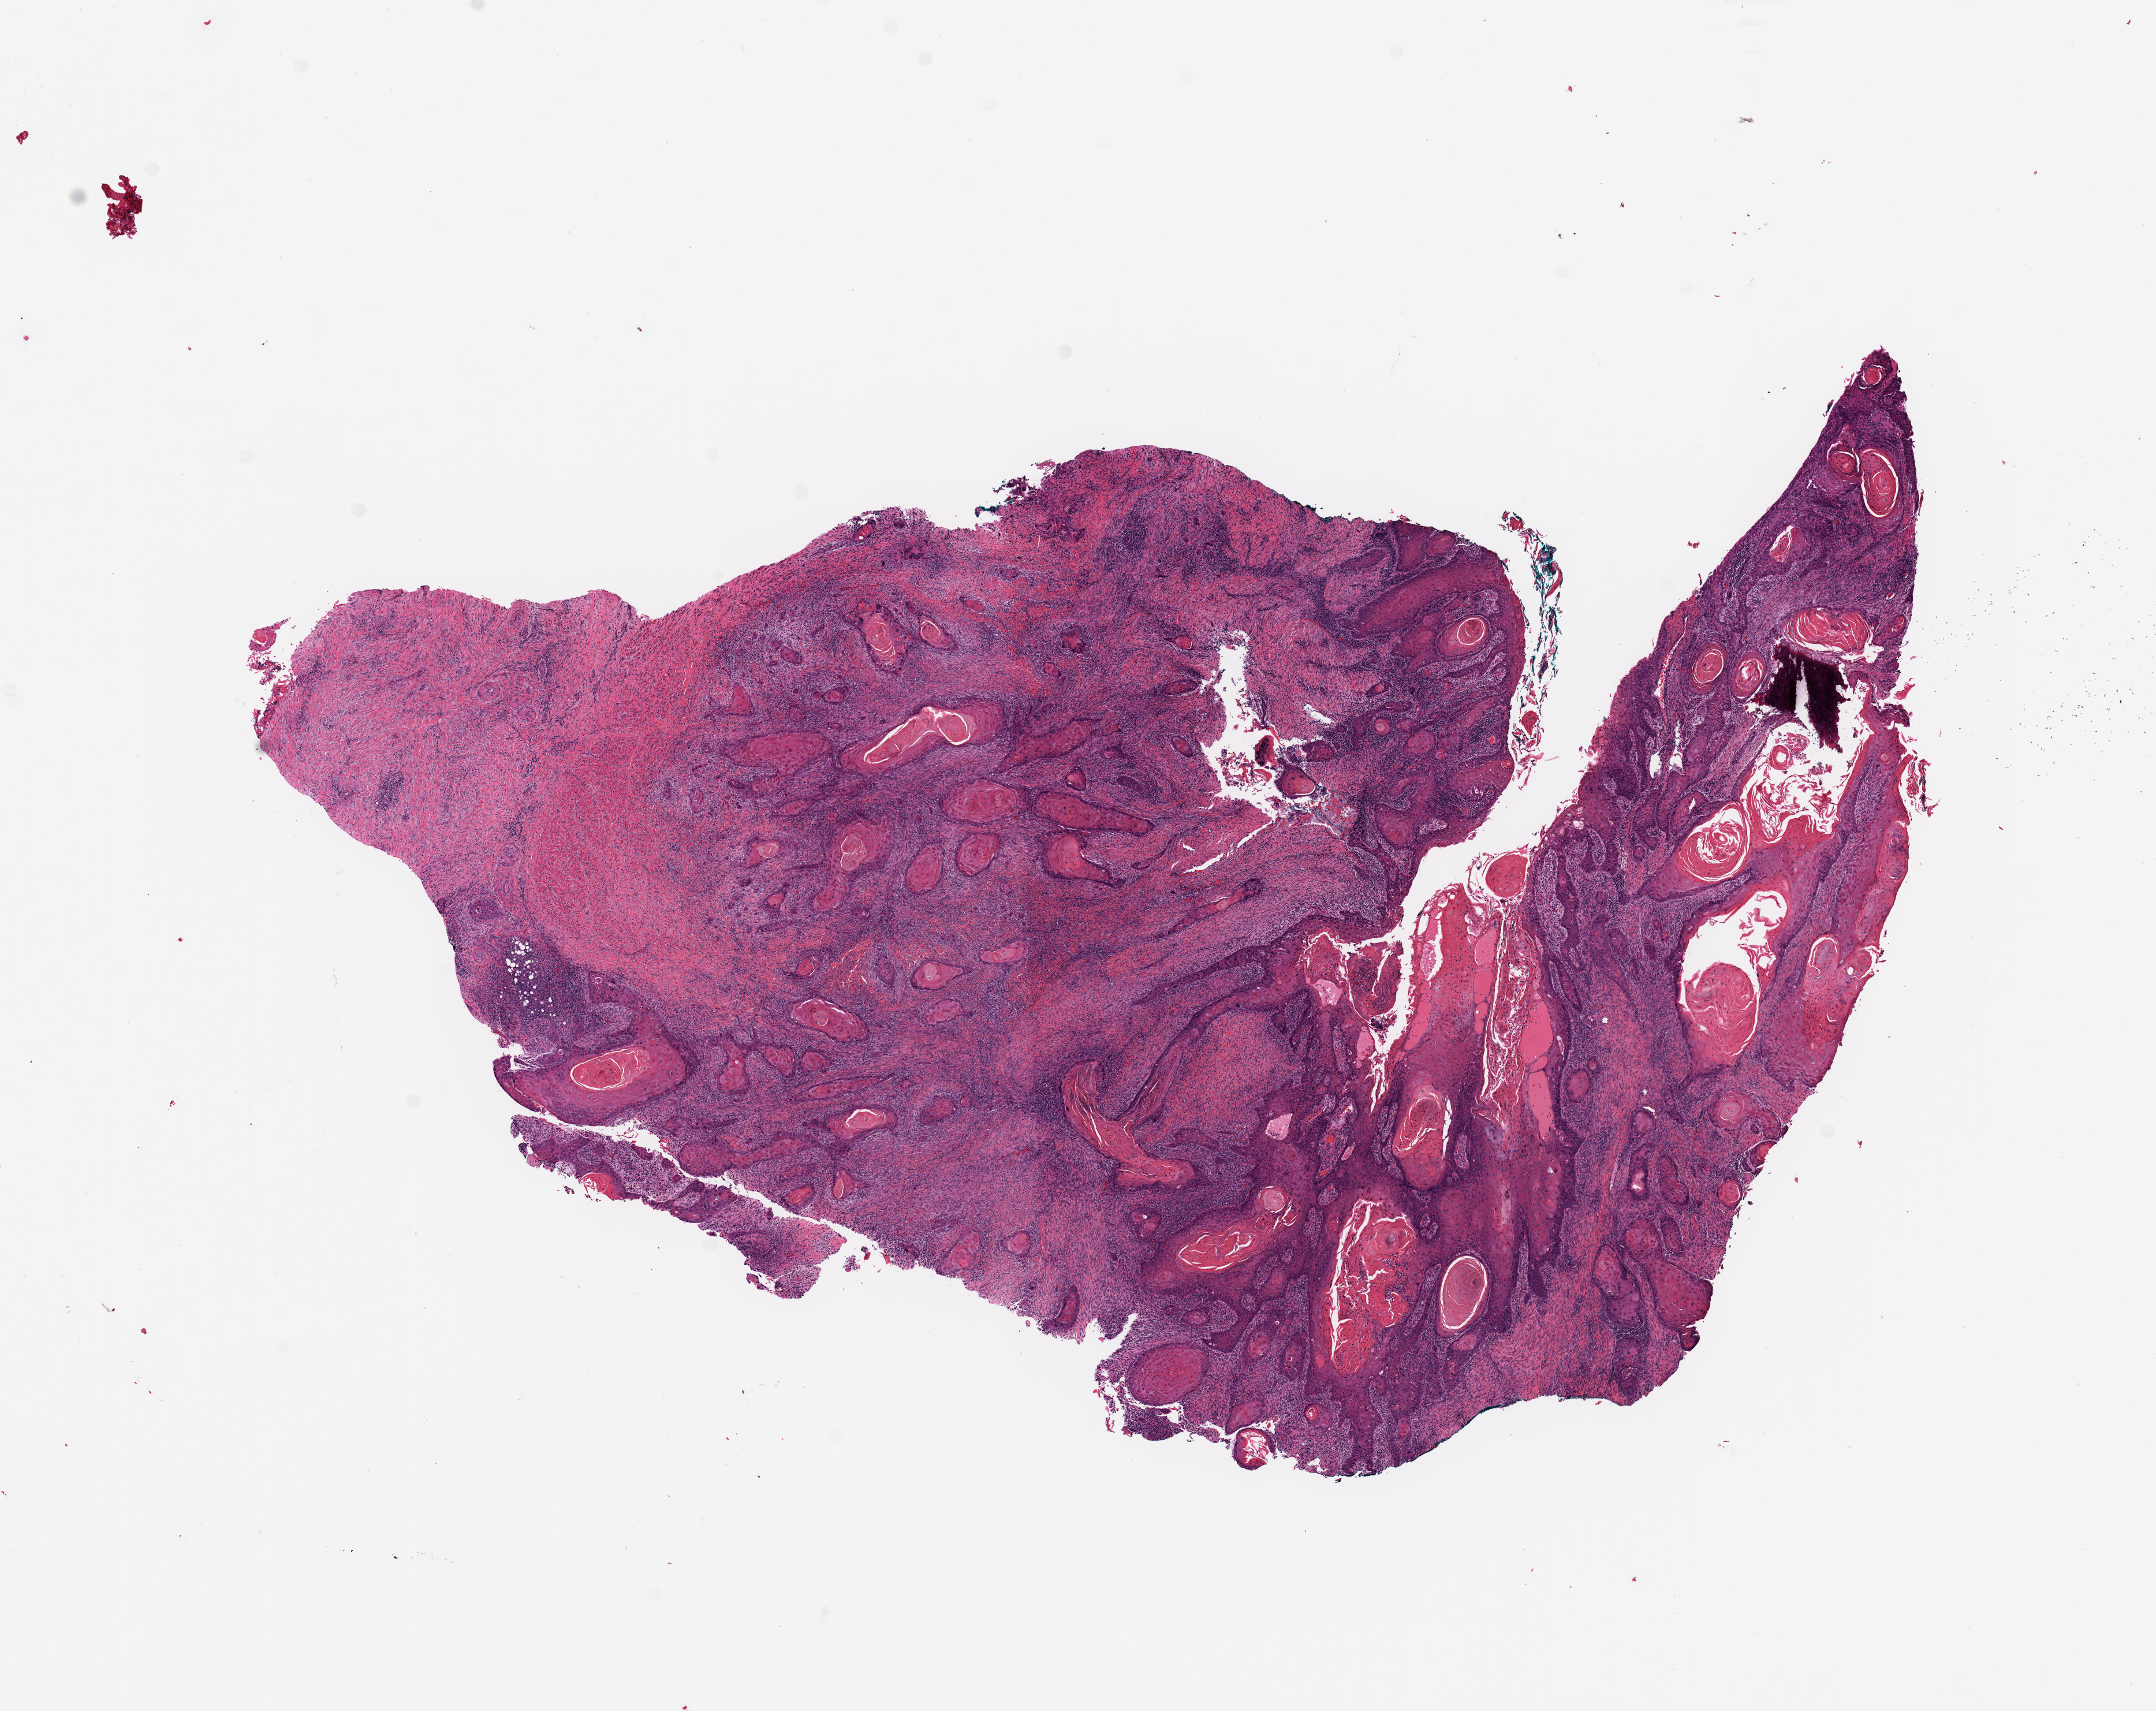
Digitized H&E tissue section (whole slide), a low-resolution overview of the entire scanned area, about 14.8 x 11.7 mm (acquisition: 20x scan). Tumour tissue sample, sampled site: buccal mucosa. Patient: male, age 56 years. Histologic grade: G1 (well differentiated). Pathologist review of this section (percent, as recorded): tumour nuclei 80%, necrosis 5%.
AJCC pathologic stage: III. Primary tumour site (as recorded): oral cavity. Histologic diagnosis: Squamous cell carcinoma, NOS.